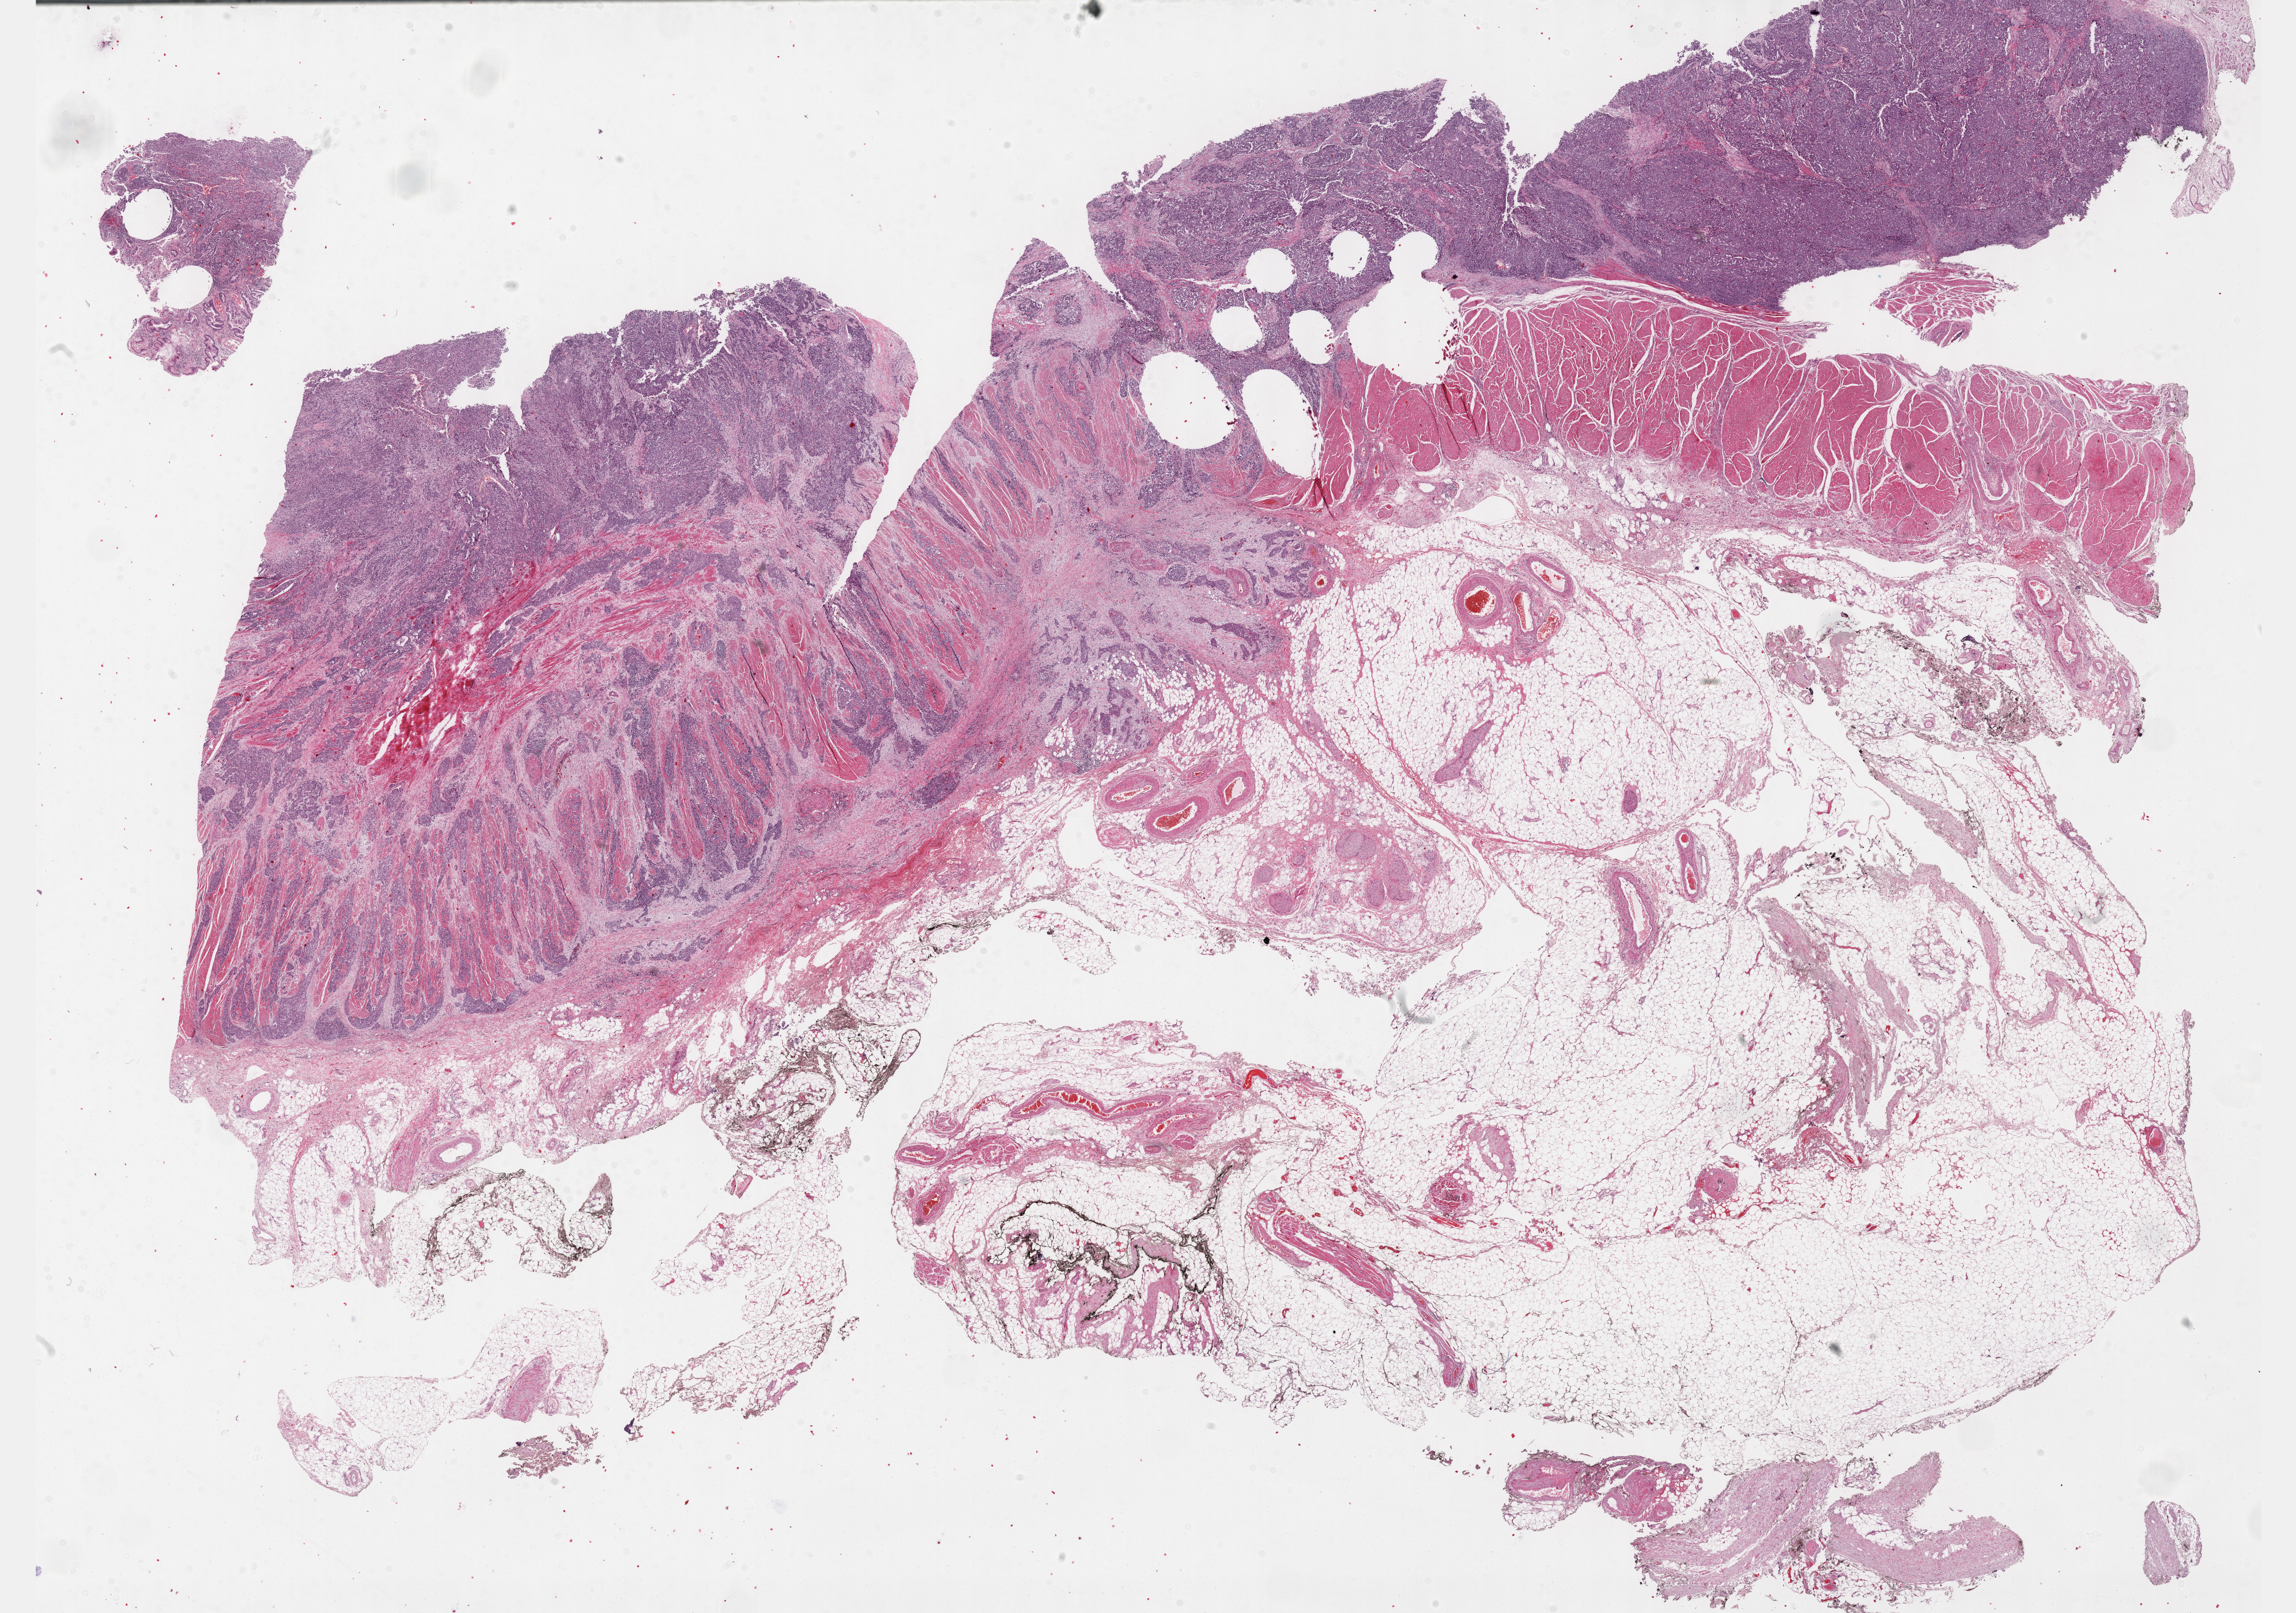
H&E-stained whole-slide image — shown as a low-resolution overview of the whole scanned area (about 32.2 x 22.6 mm); FFPE section; sample: primary tumour, esophagus. Patient: male, age at initial diagnosis 80 years.
Diagnosis: Adenocarcinoma, NOS (lower third of esophagus).